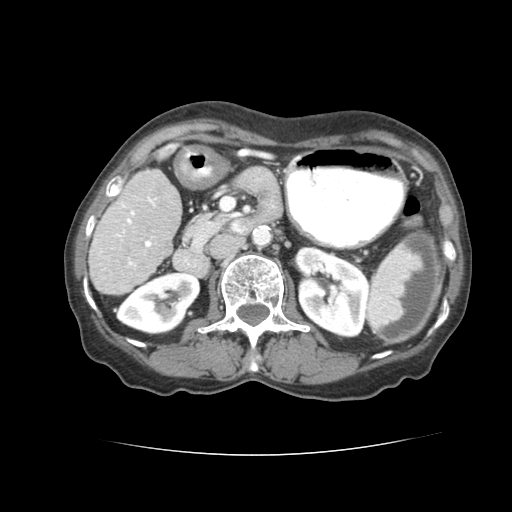
Contrast-enhanced abdominal CT (liver protocol), one axial slice; position 25 of 77 along the scan axis; soft-tissue window (W 400 / L 40 HU); 2.5 mm slice thickness; 512 × 512 image matrix, field of view 340 × 340 mm. From the clinical record (not read from this slice): diagnosis: hepatocellular carcinoma (patient treated with transarterial chemoembolisation; whether this scan precedes or follows treatment is not stated here); TNM stage (as recorded): Stage-I; Child-Pugh class: A; tumour differentiation: well differentiated; tumour nodularity: uninodular.
Structures marked on this image (semi-automatic segmentation, software-assisted and operator-edited):
- liver parenchyma outside the tumour (the mass and vessels are separate outlines, so this box may not span the whole liver): bounding box [x1, y1, x2, y2] px = [88, 168, 180, 292]
- liver vessels: [133, 193, 154, 263]